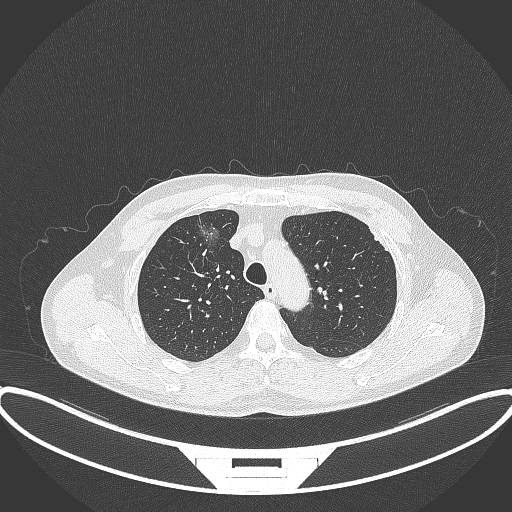
Chest CT, one axial slice; position 278 of 395 along the scan axis; lung window (W 1500 / L -600 HU); 512 × 512 image matrix, field of view 424 × 424 mm. Patient: male, 60 years. From the clinical record (not read from this slice): clinical TNM (as recorded): T1c N0 M0.
Outlined on this slice (rectangle marked by the reading radiologist):
- lung tumour (recorded histology: adenocarcinoma): bounding box [x1, y1, x2, y2] px = [194, 217, 227, 261]